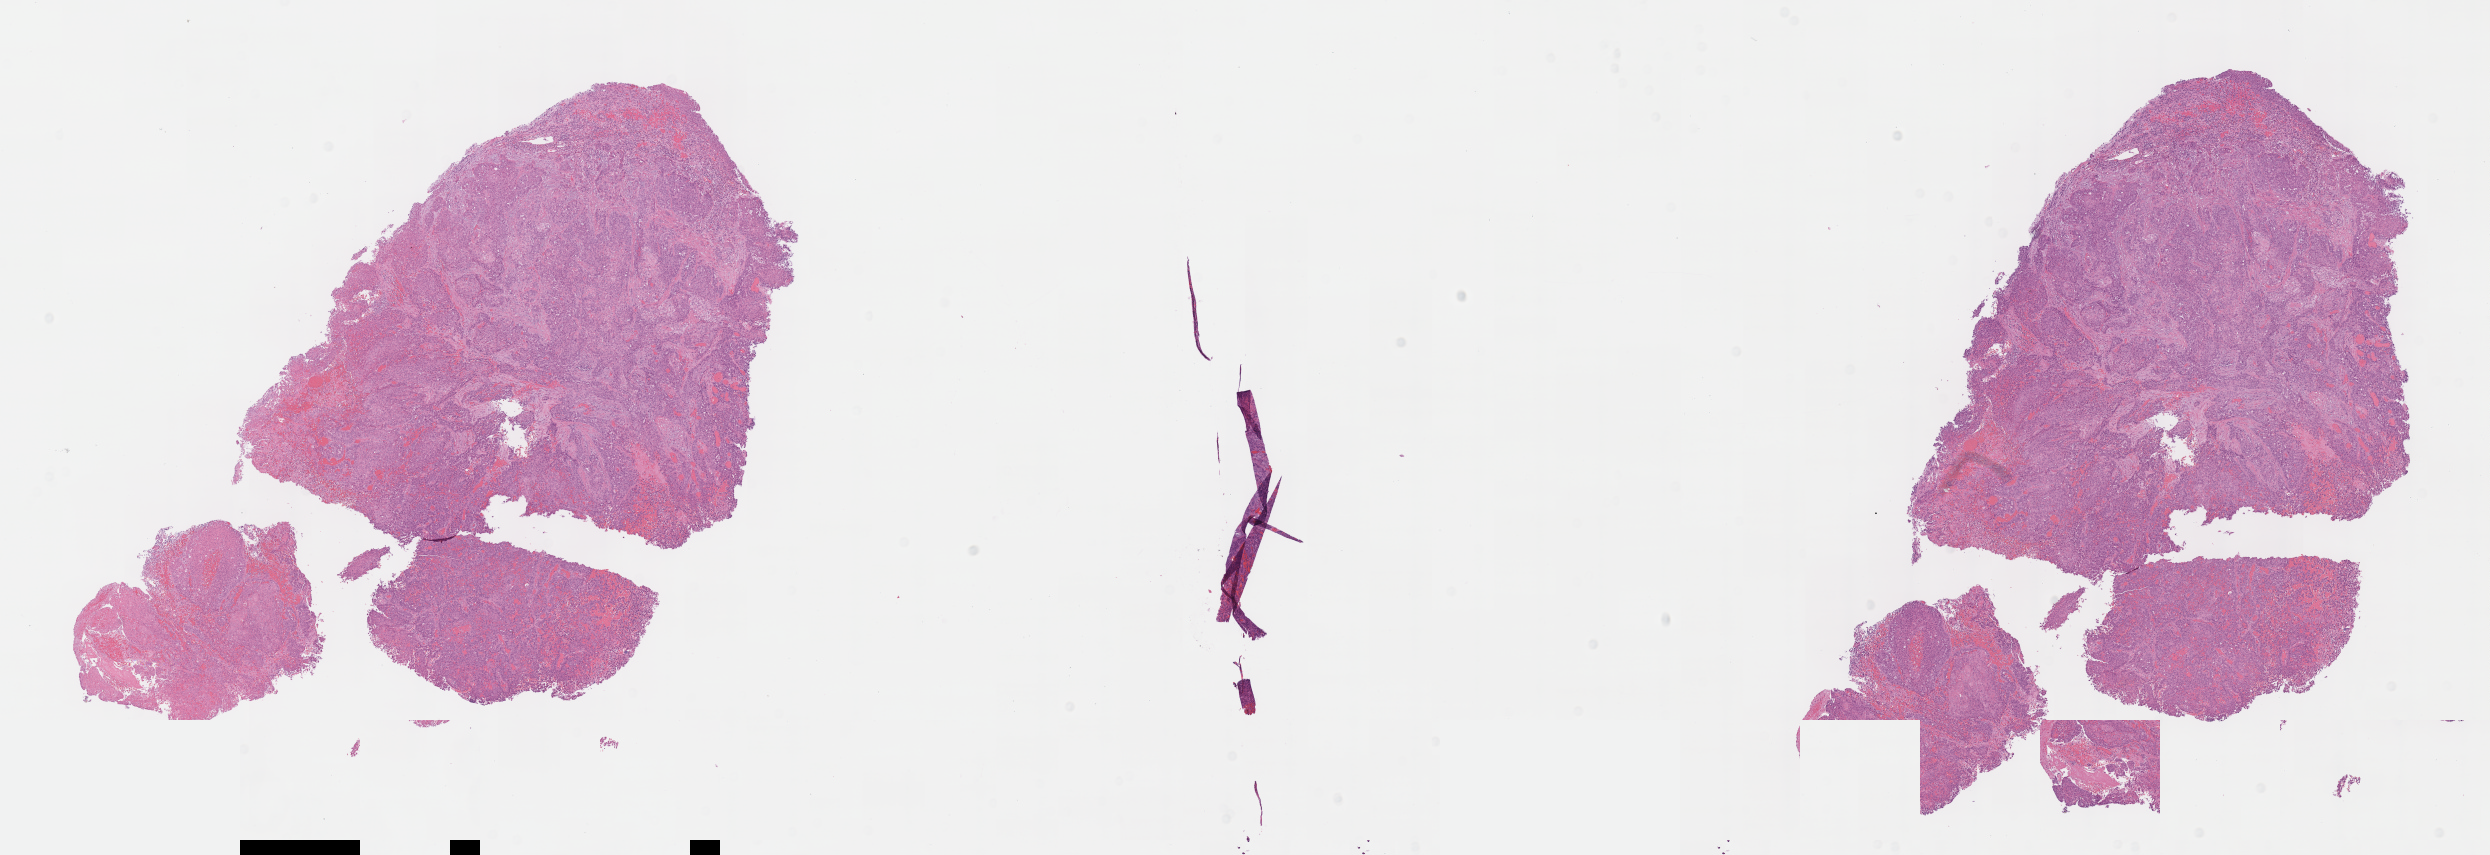
Digitized H&E-stained tissue section (whole slide) — shown as a low-resolution overview of the whole scanned area (about 19.6 x 6.7 mm), FFPE section, bladder, primary tumour sample. Female patient; age at initial diagnosis 80 years. Histologic grade: high grade.
• diagnosis: Transitional cell carcinoma
• lymph nodes positive (case pathology): 0 of 2 examined
• AJCC pathologic stage: III (7th edition)